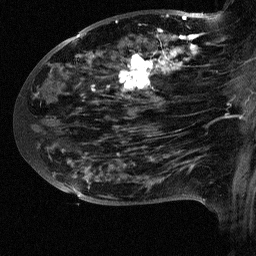
Breast MRI (dynamic contrast-enhanced), one sagittal slice; slice 33 of 64 in the series (ordered by position); dynamic contrast-enhanced study with each time point stored as its own series, time point 2 of 3 at this slice position (early post-contrast, ordered by acquisition time); 1.5 T; TE 4.5 ms, TR 11 ms; 2.5 mm slice thickness; 256 × 256 image matrix. Female patient, age 38 years. Case-level facts recorded for this patient, not image findings: setting: breast cancer imaged before/during neoadjuvant chemotherapy; receptor status: HR-positive, HER2-negative.
Structures marked on this image (semi-automatic segmentation, software-assisted and operator-edited):
- analysis volume of interest (the breast-tissue region the enhancement analysis was run in; not a lesion): bounding box <88,18,252,126> (left, top, right, bottom; pixels)
- tumour enhancement mask (voxels above the 90 % enhancement threshold inside the analysis volume of interest): <92,18,241,118>